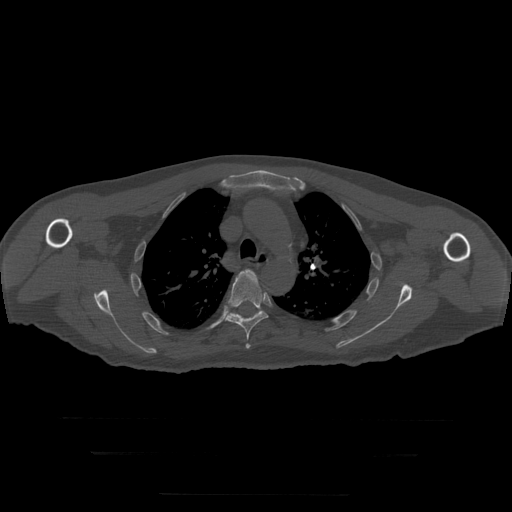
CT including the spine, one axial slice; slice 224 of 397 in the series (ordered by position); bone window (W 1800 / L 400 HU); 1.25 mm slice thickness; 512 × 512 image matrix, field of view 510 × 510 mm. Patient age 73 years. From the clinical record (not read from this slice): primary cancer: prostate.
Annotated regions visible in this slice (semi-automatically segmented with operator editing):
- T4 vertebra: bounding box [x1, y1, x2, y2] px = [243, 269, 256, 277]
- T5 vertebra: [225, 271, 268, 349]
- T6 vertebra: [230, 311, 261, 319]